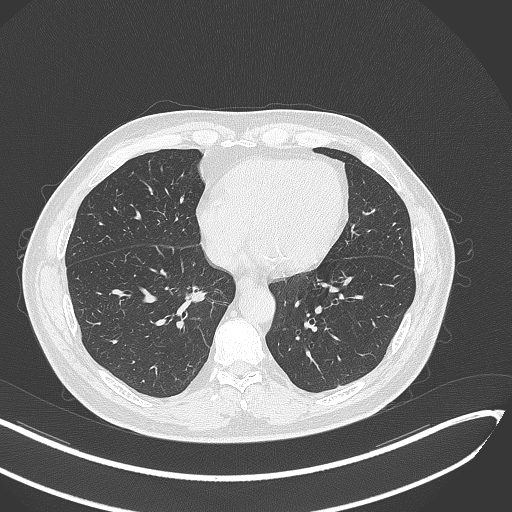
Chest CT, one axial slice. Slice 136 of 429 in the series (ordered by position). Reconstruction kernel B70f. 120 kVp. Lung window (W 1500 / L -600 HU). 1 mm slice thickness. 512 × 512 image matrix. Patient: male, 62 years. Case-level facts recorded for this patient, not image findings: clinical TNM (as recorded): T1b N0 M0; histopathological grade: G2.
Structures marked on this image (bounding box drawn by a radiologist):
- lung tumour (recorded histology: adenocarcinoma): box from (x=180, y=281) to (x=212, y=306) px